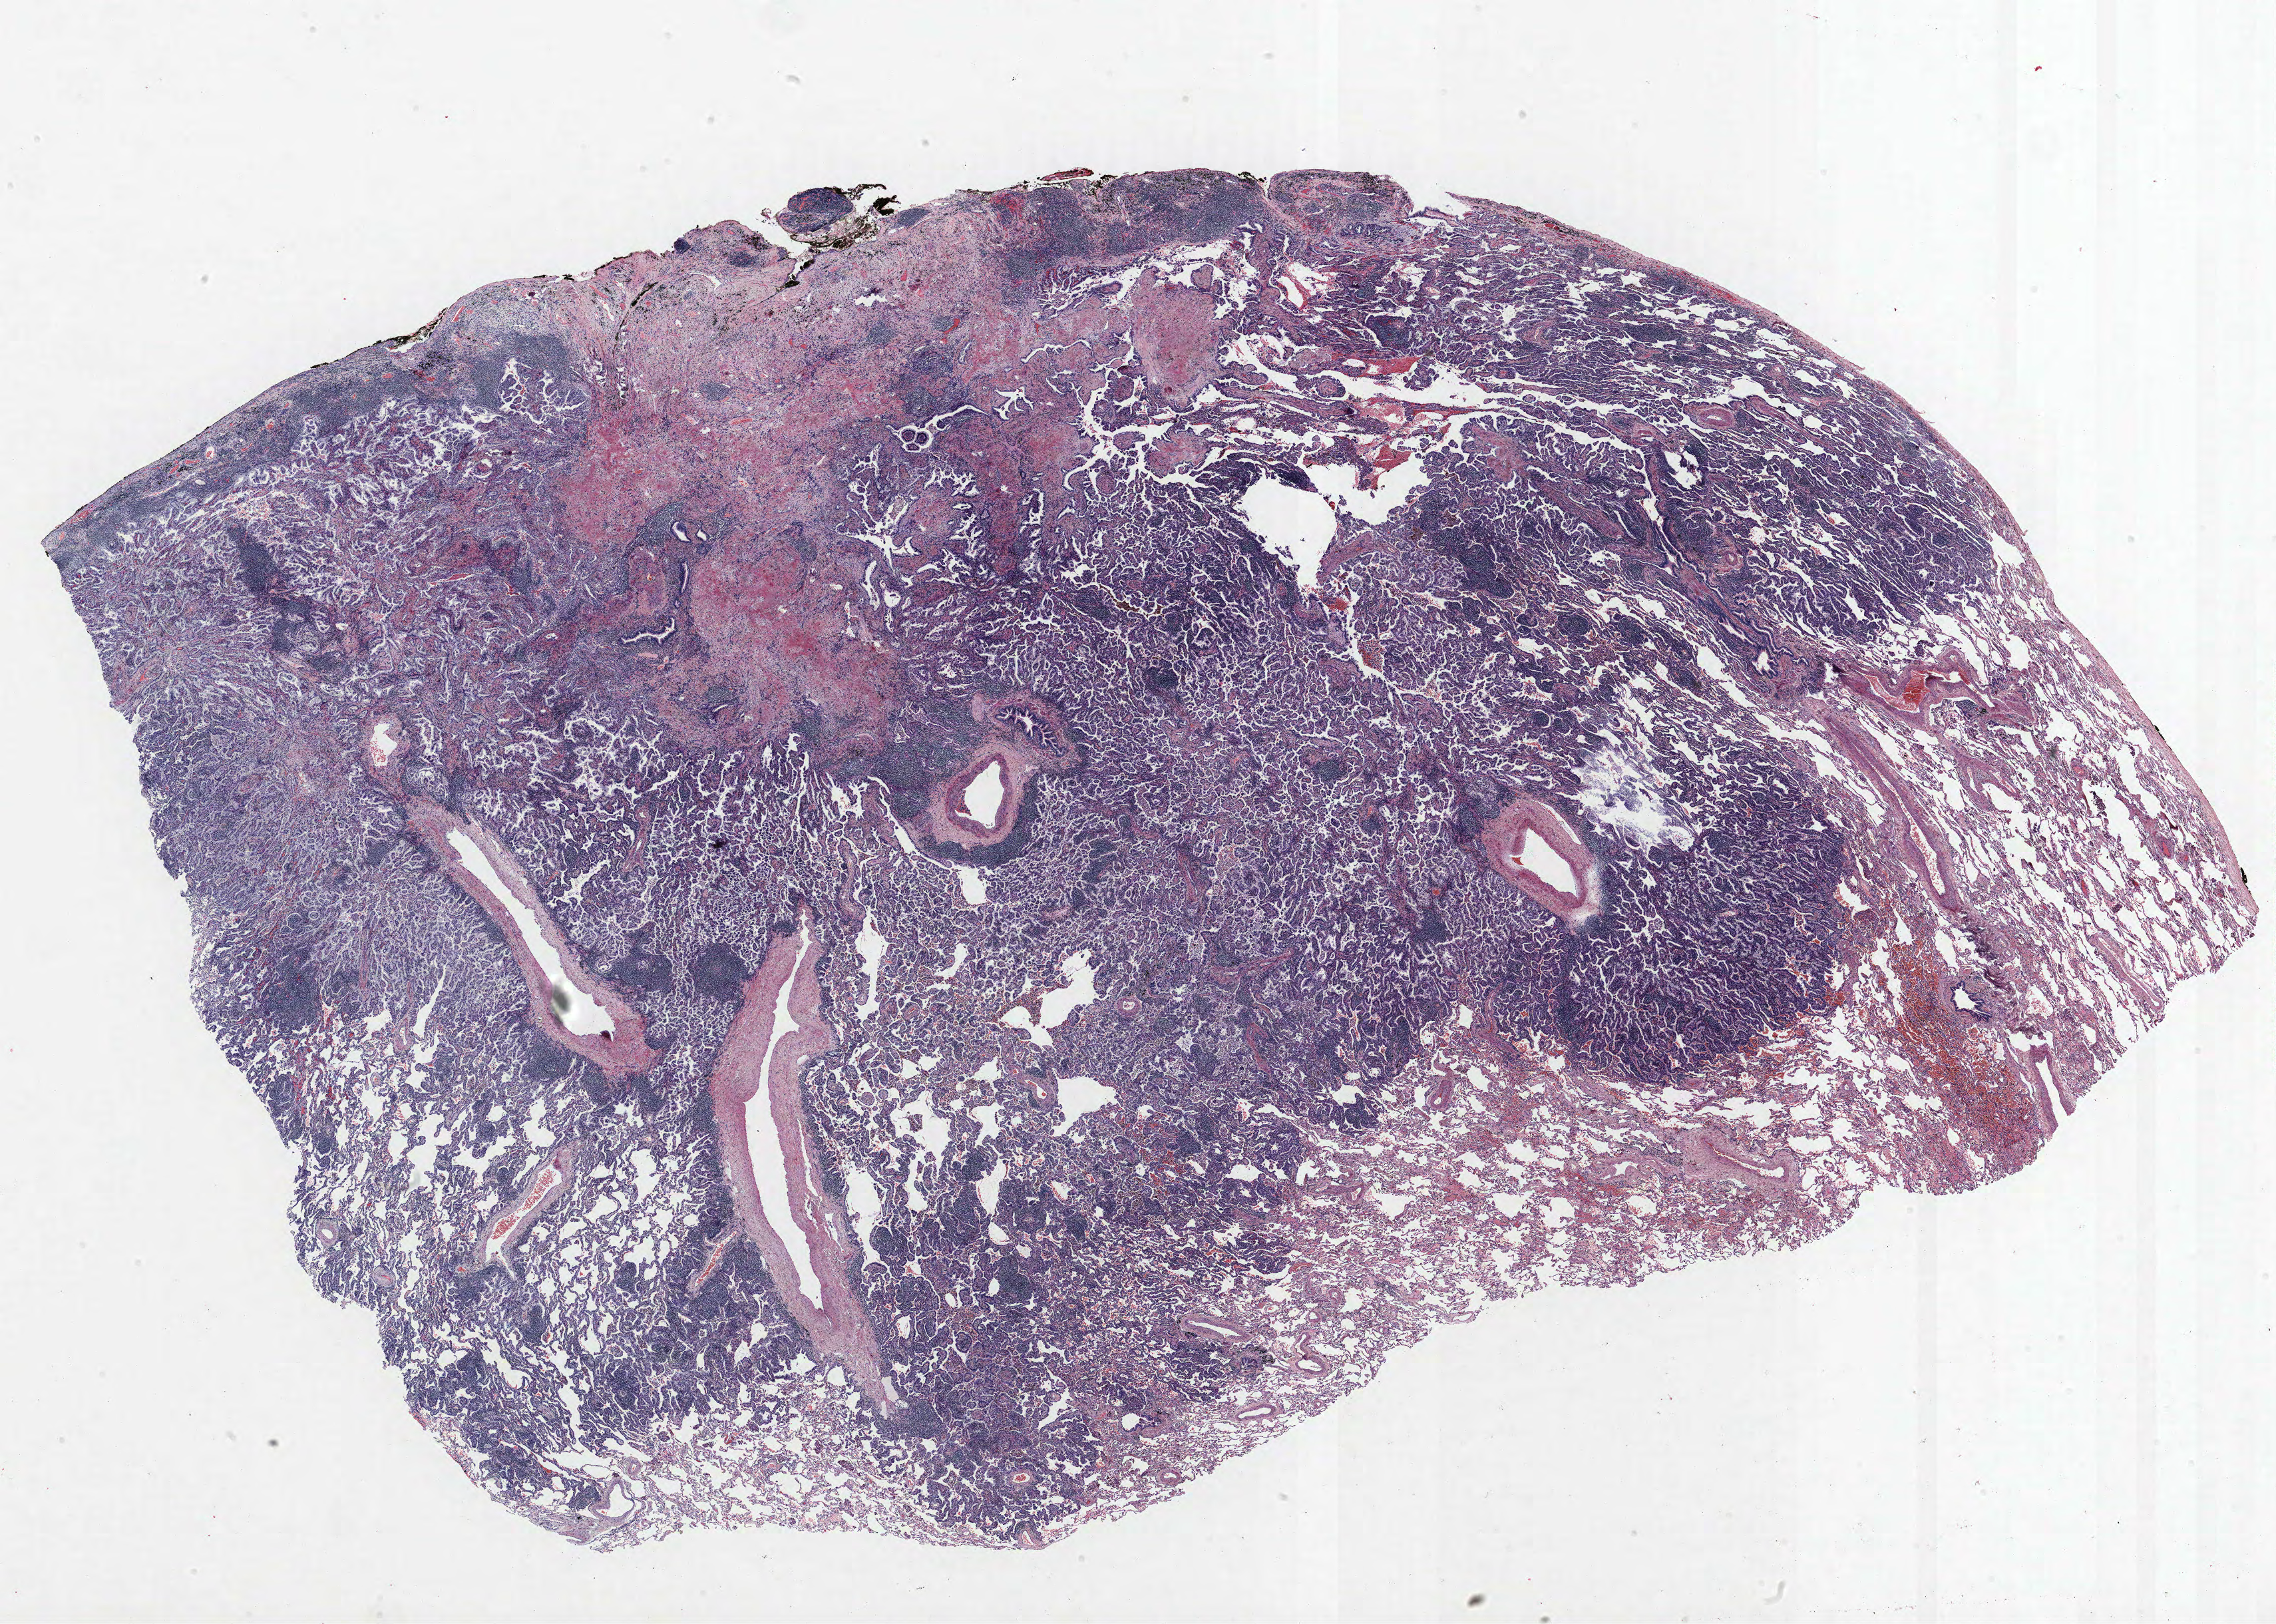
H&E whole-slide image, whole scanned area (about 27.4 x 19.5 mm, from a 40x scan) shown as a low-resolution overview; FFPE section; lung tissue. Male, age 60 at enrolment. Current smoker at enrolment. Grade: well differentiated (G1).
Participant's lung-cancer diagnosis: Bronchiolo-alveolar adenocarcinoma, NOS (ICD-O-3 8250/3). Primary tumour location (clinical record): left upper lobe. Stage (AJCC 6th edition): IA. Tumour size (pathology): 27 mm.